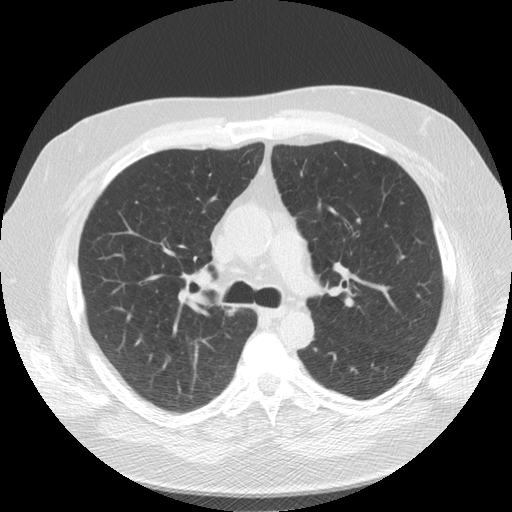
Low-dose screening chest CT, one axial slice. Position 93 of 136 along the scan axis. Reconstruction kernel STANDARD. Lung window (W 1500 / L -600 HU). 2.5 mm slice thickness. 512 × 512 image matrix, field of view 360 × 360 mm.
Outlined on this slice (expert manual segmentation):
- lesion 1 (tumor, upper lobe of right lung): bounding box [x1, y1, x2, y2] px = [225, 308, 239, 317]